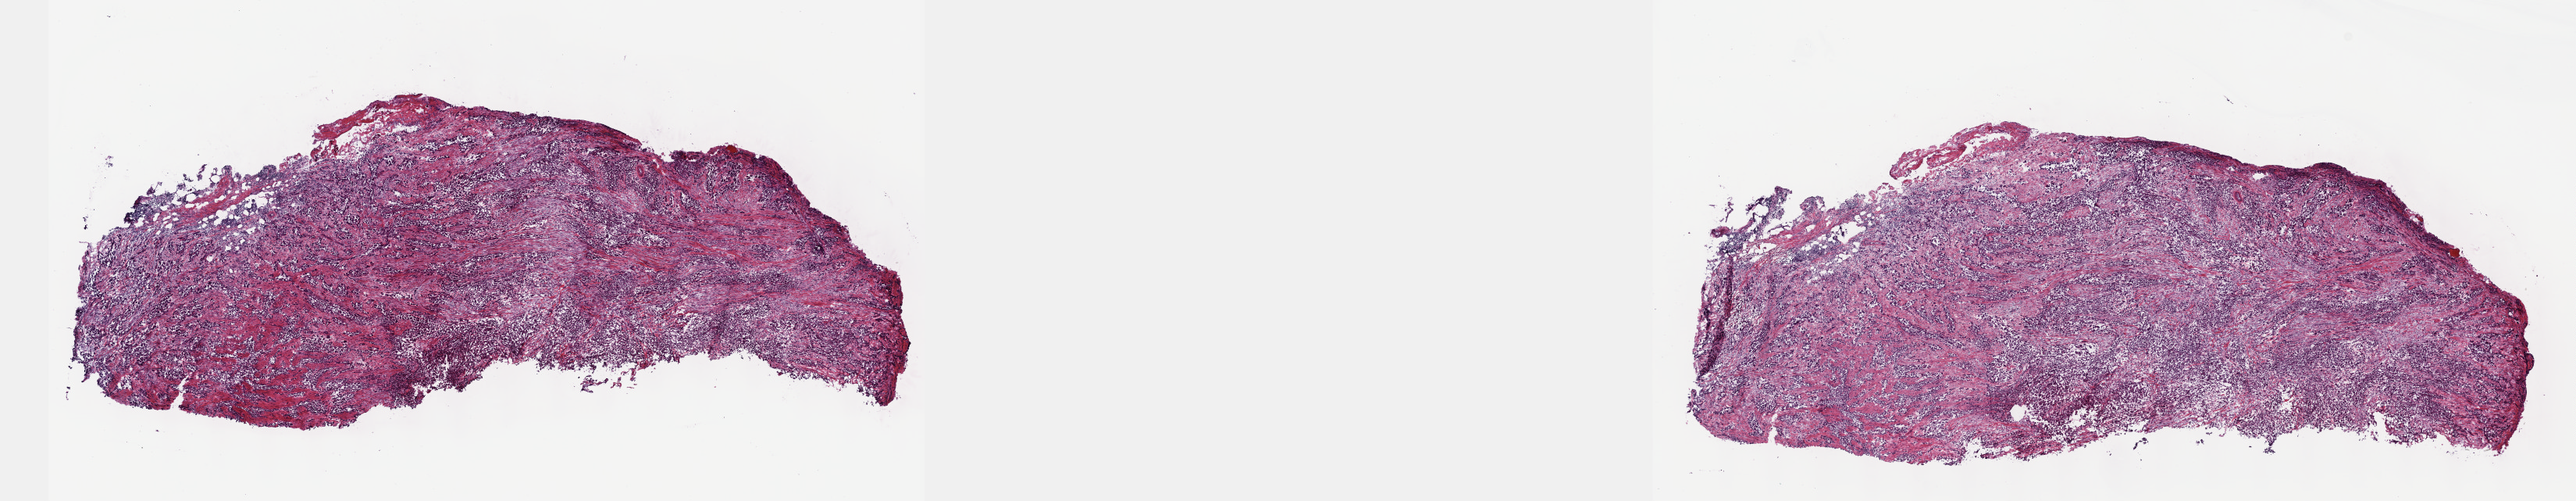
Whole-slide histology image, Hematoxylin and eosin (H&E) stained — shown as a low-resolution overview of the whole scanned area (about 26.7 x 5.2 mm), frozen section from the top of the tissue portion, primary tumour sample from the mesothelium. Male, age 69 years at initial diagnosis. Slide review estimates, as recorded: tumour cells 100%, tumour nuclei 65%, normal cells 0%, stromal cells 0%, necrosis 0%. Inflammatory infiltration, as recorded: lymphocyte infiltration 0%, monocyte infiltration 0%, neutrophil infiltration 0%.
AJCC pathologic stage: III (6th edition). Laterality: right. Histologic diagnosis: Epithelioid mesothelioma, malignant (pleura, NOS).